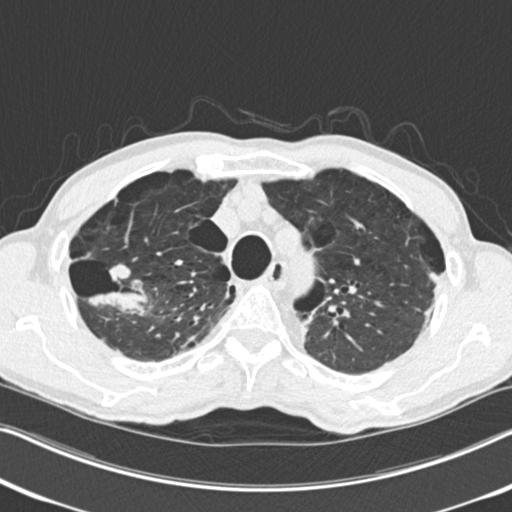
Low-dose screening chest CT, axial slice, second screening round (one year after baseline), lung window (W 1500 / L -600 HU), 120 kVp, 512 × 512 image matrix, field of view 334 × 334 mm. Male, age 71 years at enrolment. Current smoker at enrolment.
Expert reader's lesion annotation, bounding box (x1, y1, x2, y2) in pixels: (76, 254, 150, 320). The screening reader recorded 4 non-calcified nodules or masses ≥4 mm on this exam (right upper lobe, right upper lobe, right upper lobe, left upper lobe); which of them this box marks is not recorded. Participant outcome: lung cancer diagnosed 83 days after this screen — adenocarcinoma, NOS, right upper lobe, well differentiated (G1), stage IA (AJCC 6th edition), 30 mm at pathology.